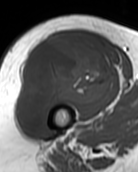
MRI of an extremity soft-tissue mass, one axial slice. Position 63 of 99 along the scan axis. MR volume resampled by the dataset authors to the PET/CT grid (not the native acquisition matrix). 3.27 mm slice thickness. 138 × 172 image matrix, field of view 135 × 168 mm. Female patient. From the clinical record (not read from this slice): histological type: pleiomorphic undifferentiated sarcoma; grade: high; site of the primary tumour: right quadricep.
Annotated regions visible in this slice (expert contour drawn on MRI and transferred to this co-registered scan by the dataset authors):
- gross tumour volume including surrounding oedema: bounding box [x1, y1, x2, y2] px = [16, 36, 116, 129]
- gross tumour volume (mass): [16, 36, 116, 129]